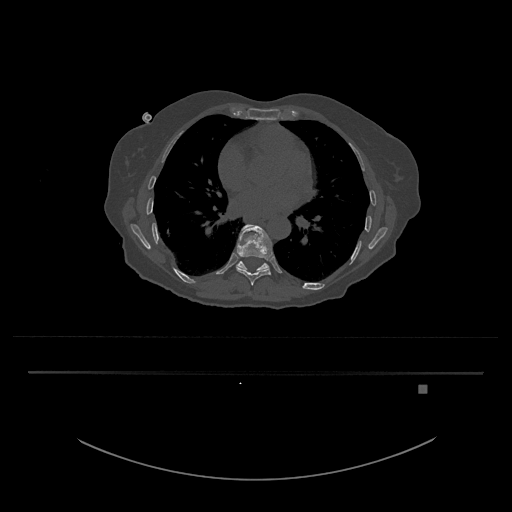
CT including the spine, one axial slice. Position 747 of 797 along the scan axis. Reconstruction kernel Br40s/3. Bone window (W 1800 / L 400 HU). 0.5 mm slice thickness. 512 × 512 image matrix. Patient: female, 57 years. From the clinical record (not read from this slice): primary cancer: cervical.
Structures marked on this image (semi-automatically segmented with operator editing):
- T10 vertebra: bounding box [x1, y1, x2, y2] px = [236, 261, 270, 272]
- T9 vertebra: [236, 224, 273, 286]